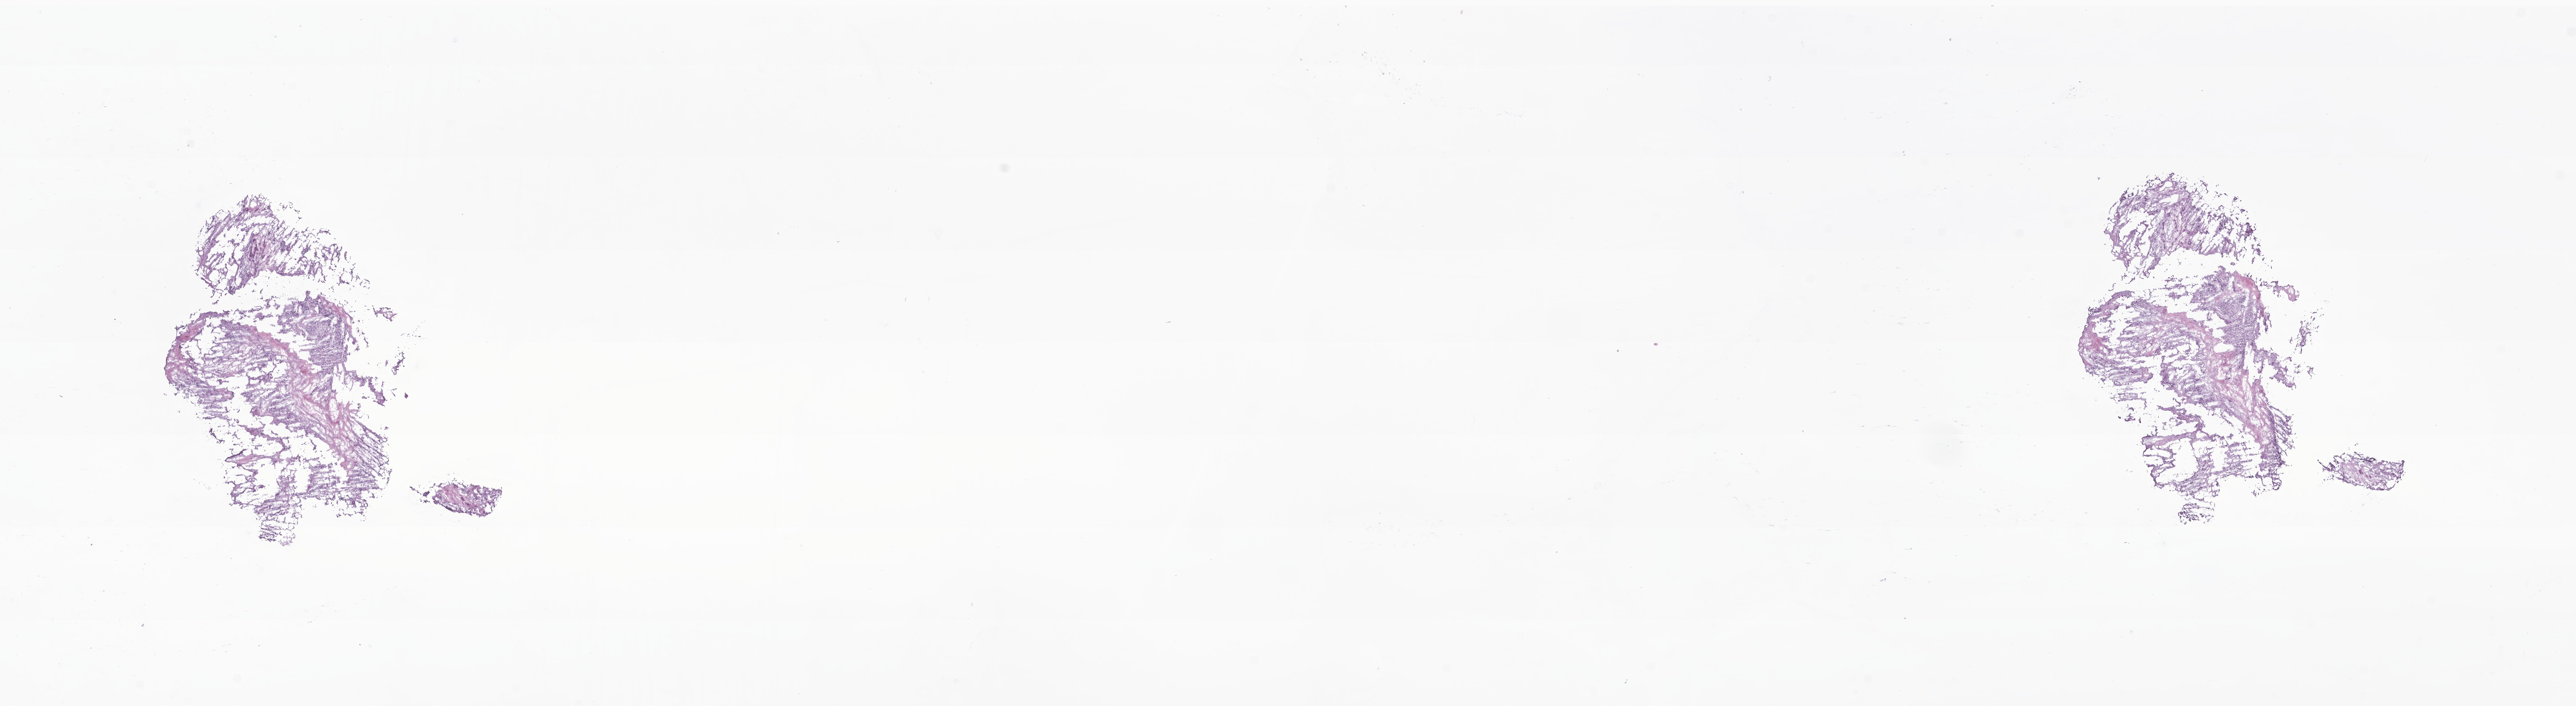
Digitized hematoxylin and eosin (H&E)-stained section of tumor tissue from the retroperitoneum — shown as a low-resolution overview of the whole scanned area (about 29.8 x 8.2 mm). Frozen section (OCT-embedded). Patient: male, age 923 days (about 2.5 years).
• recorded diagnosis: Neuroblastoma, NOS